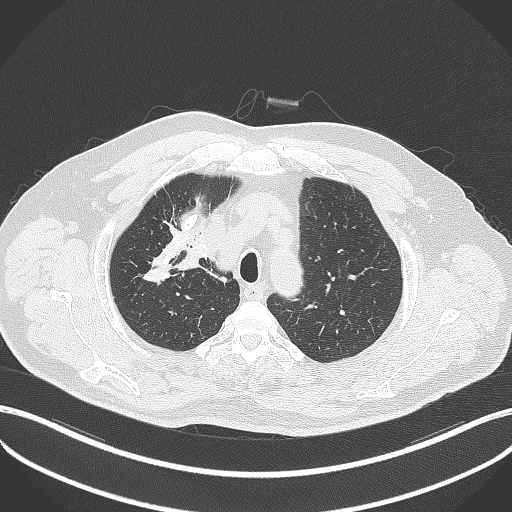
Chest CT, one axial slice; position 314 of 411 along the scan axis; lung window (W 1500 / L -600 HU); 1 mm slice thickness; 512 × 512 image matrix, field of view 400 × 400 mm. Male patient, age 60 years. Case-level facts recorded for this patient, not image findings: clinical TNM (as recorded): T1b N1 M0.
Outlined on this slice (rectangle marked by the reading radiologist):
- lung tumour (recorded histology: squamous cell carcinoma): bounding box (x1, y1, x2, y2) in pixels: (173, 247, 206, 275)